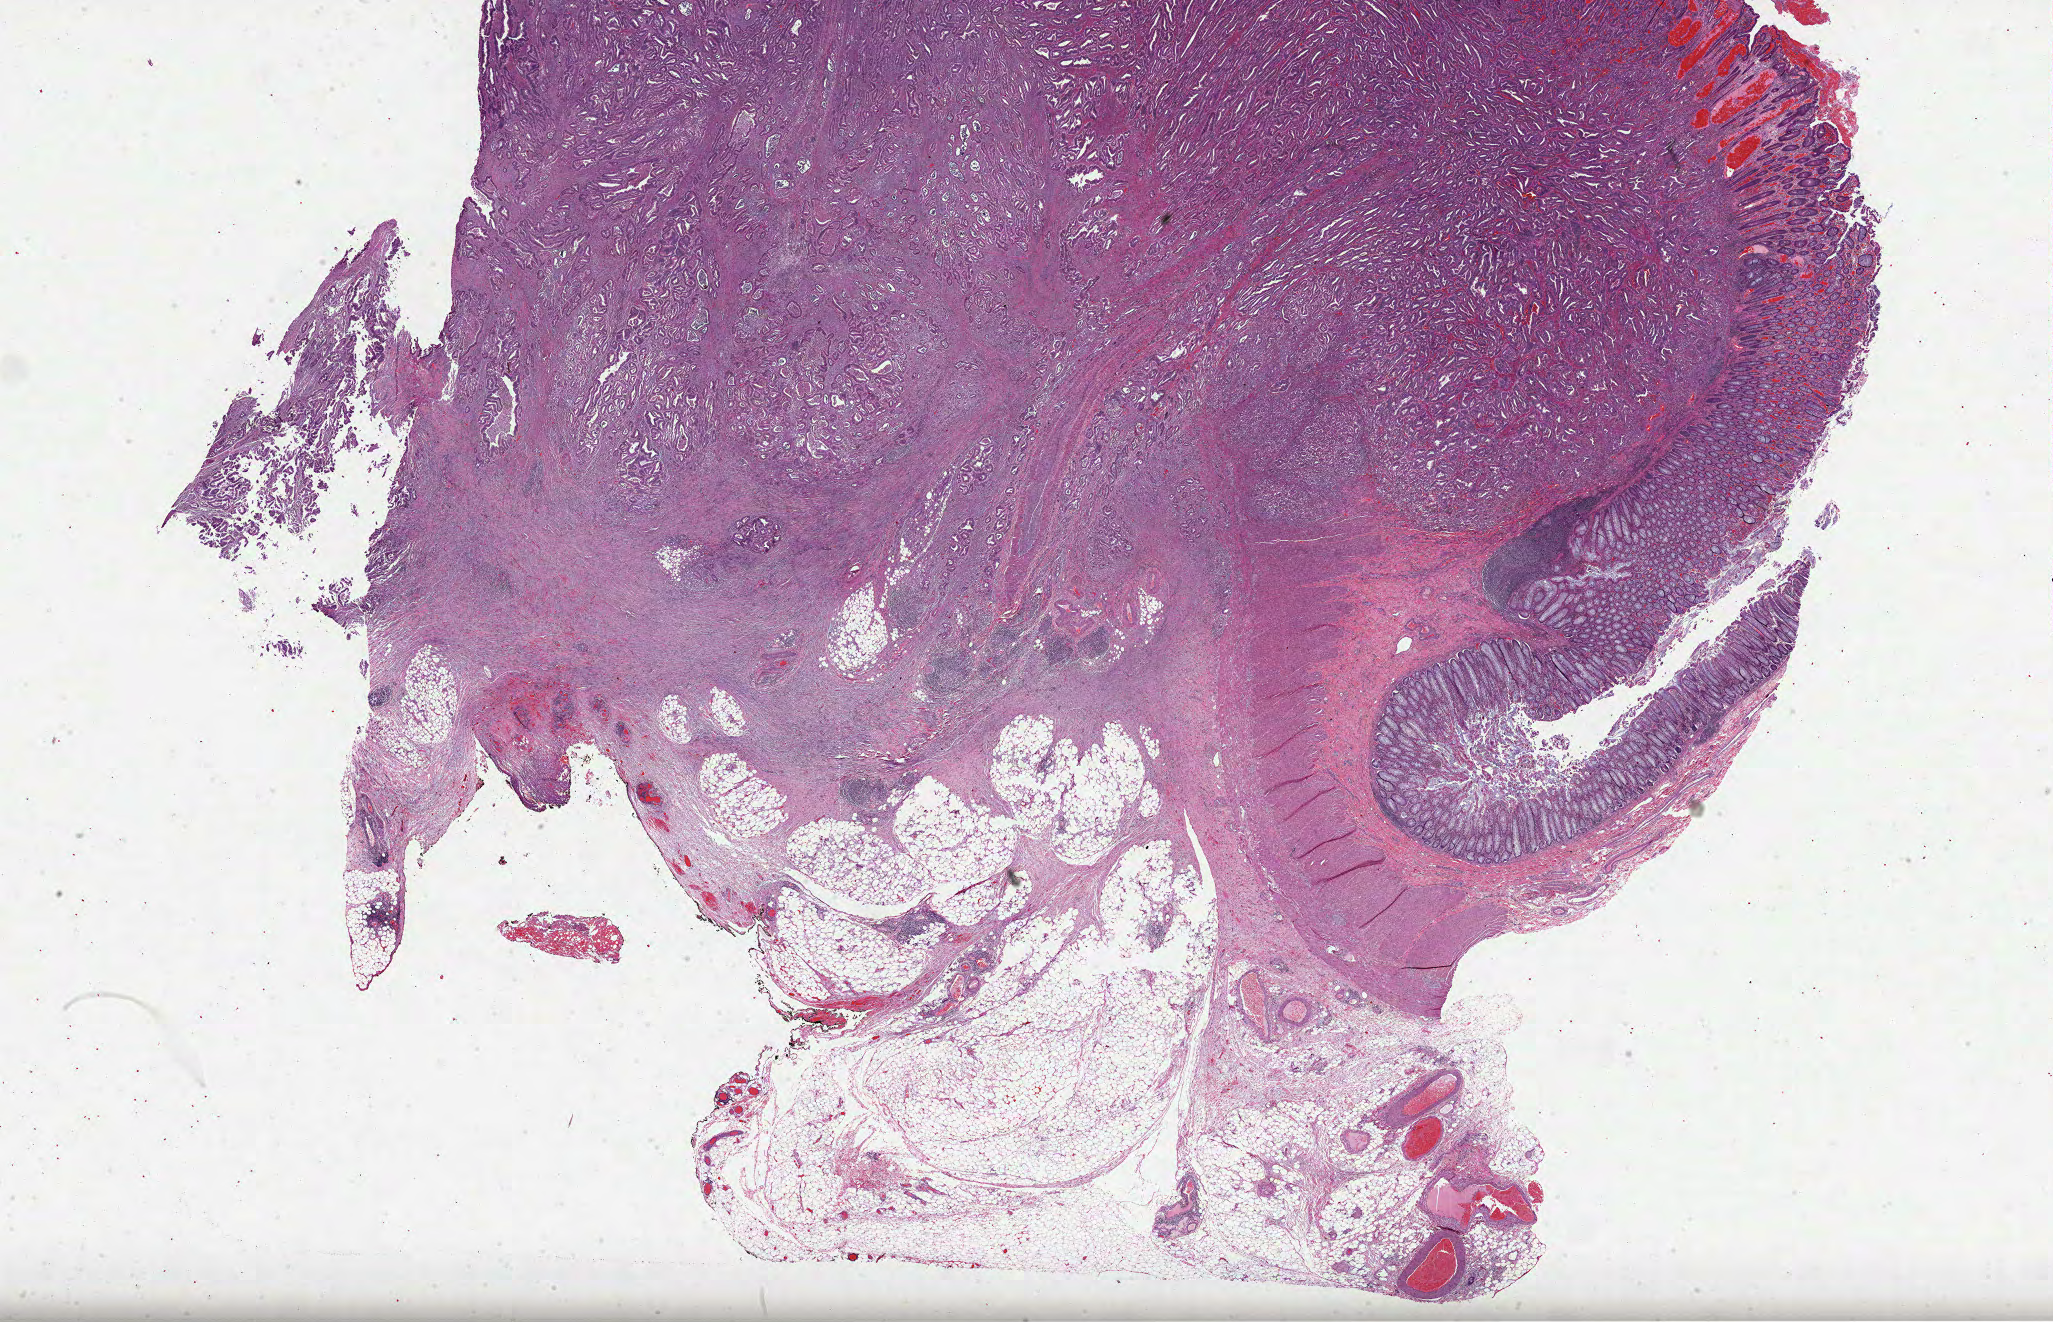
Whole-slide histology image, Hematoxylin and eosin (H&E) stained — a low-resolution overview of the entire scanned area, about 33.1 x 21.3 mm (acquisition: 40x scan). Formalin-fixed paraffin-embedded (FFPE) diagnostic section. Sample: primary tumour, colon. Patient: male, age at initial diagnosis 35 years.
Diagnosis: Adenocarcinoma, NOS.